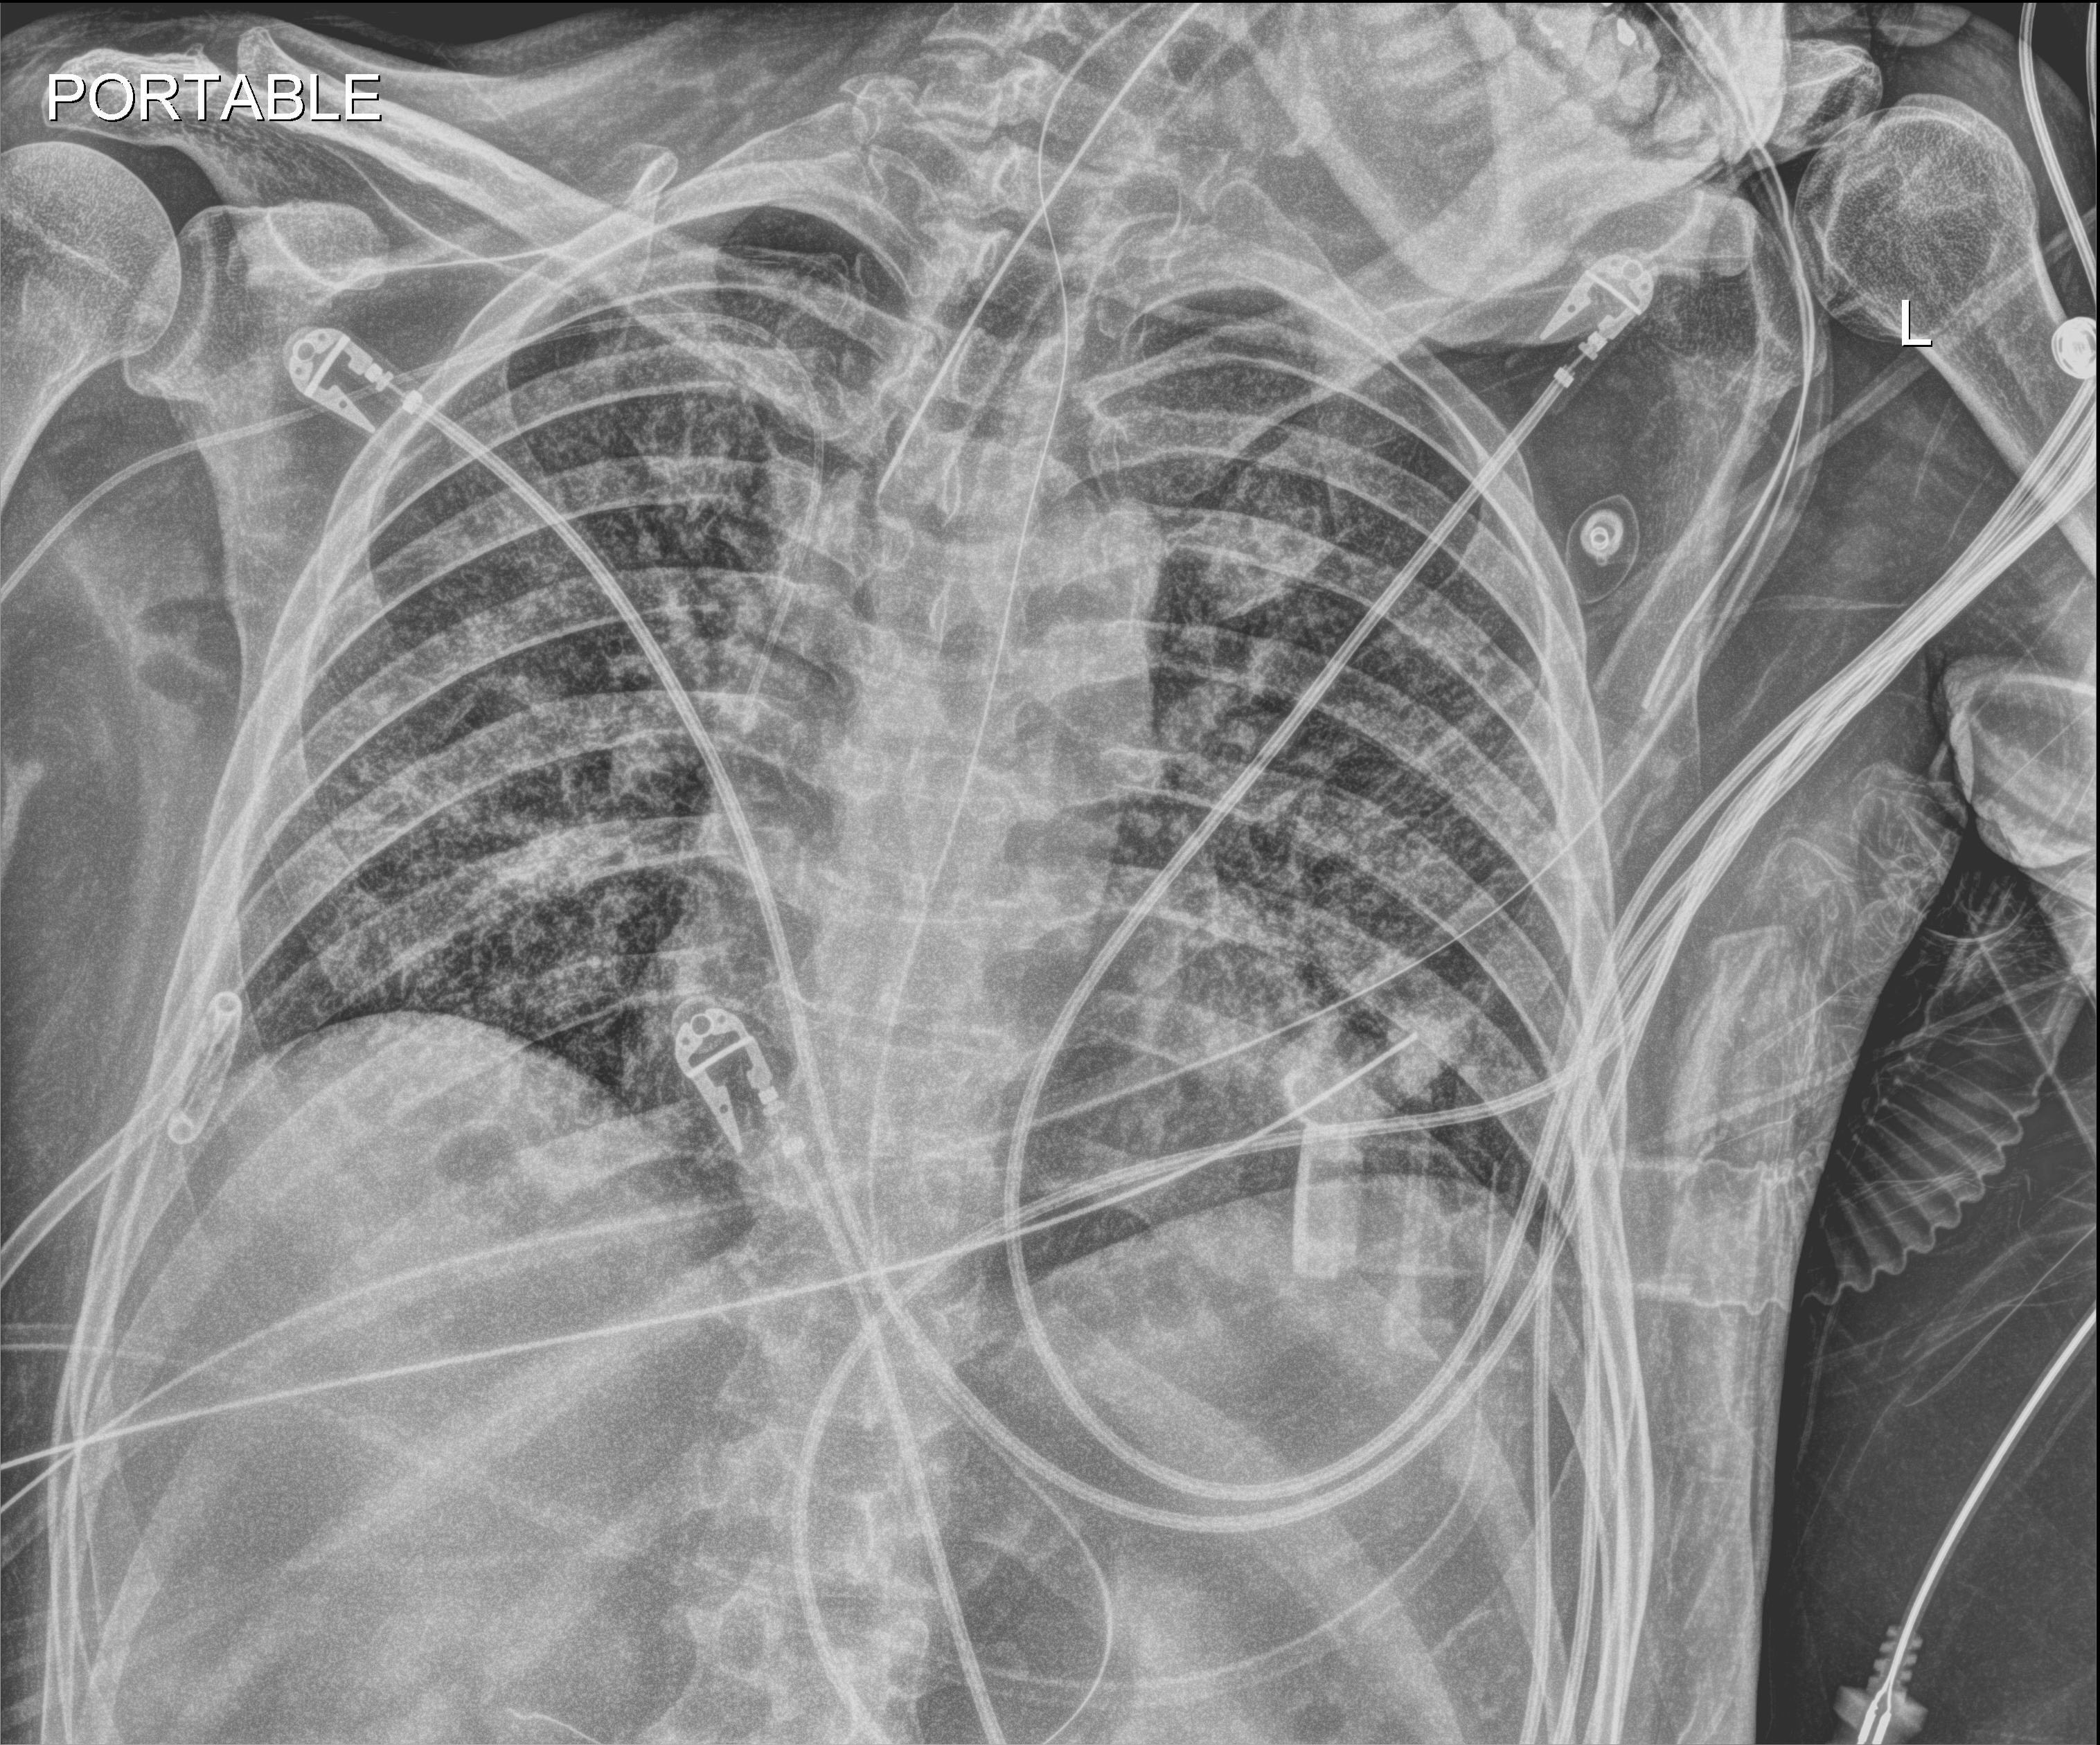
Bedside chest radiograph (digital radiography); anteroposterior (AP) projection. Patient hospitalised with COVID-19; male, aged 18–59 years.
From the hospital-stay record, not from the radiograph (when in the stay this image was taken is not recorded): mechanically ventilated during this hospital stay: yes.